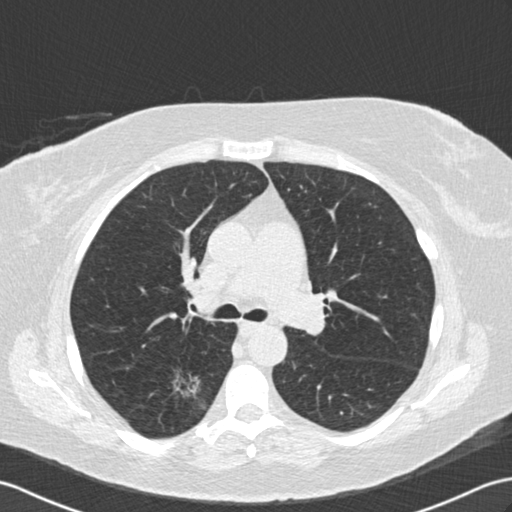
Low-dose screening chest CT, one axial slice; position 99 of 154 along the scan axis; 120 kVp; lung window (W 1500 / L -600 HU); 512 × 512 image matrix.
Outlined on this slice (expert manual segmentation):
- lesion 1 (tumor, lower lobe of right lung): box from (x=173, y=372) to (x=201, y=399) px